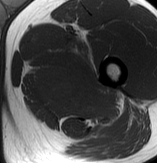
MRI of an extremity soft-tissue mass, one axial slice. Position 61 of 70 along the scan axis. MR volume resampled by the dataset authors to the PET/CT grid (not the native acquisition matrix). 3.27 mm slice thickness. 157 × 163 image matrix, field of view 153 × 159 mm. Male patient. Case-level facts recorded for this patient, not image findings: histological type: extraskeletal osteosarcoma; grade: high; site of the primary tumour: left adductur.
Annotated regions visible in this slice (expert contour drawn on MRI and transferred to this co-registered scan by the dataset authors):
- gross tumour volume (mass): bounding box <33,35,121,127> (left, top, right, bottom; pixels)